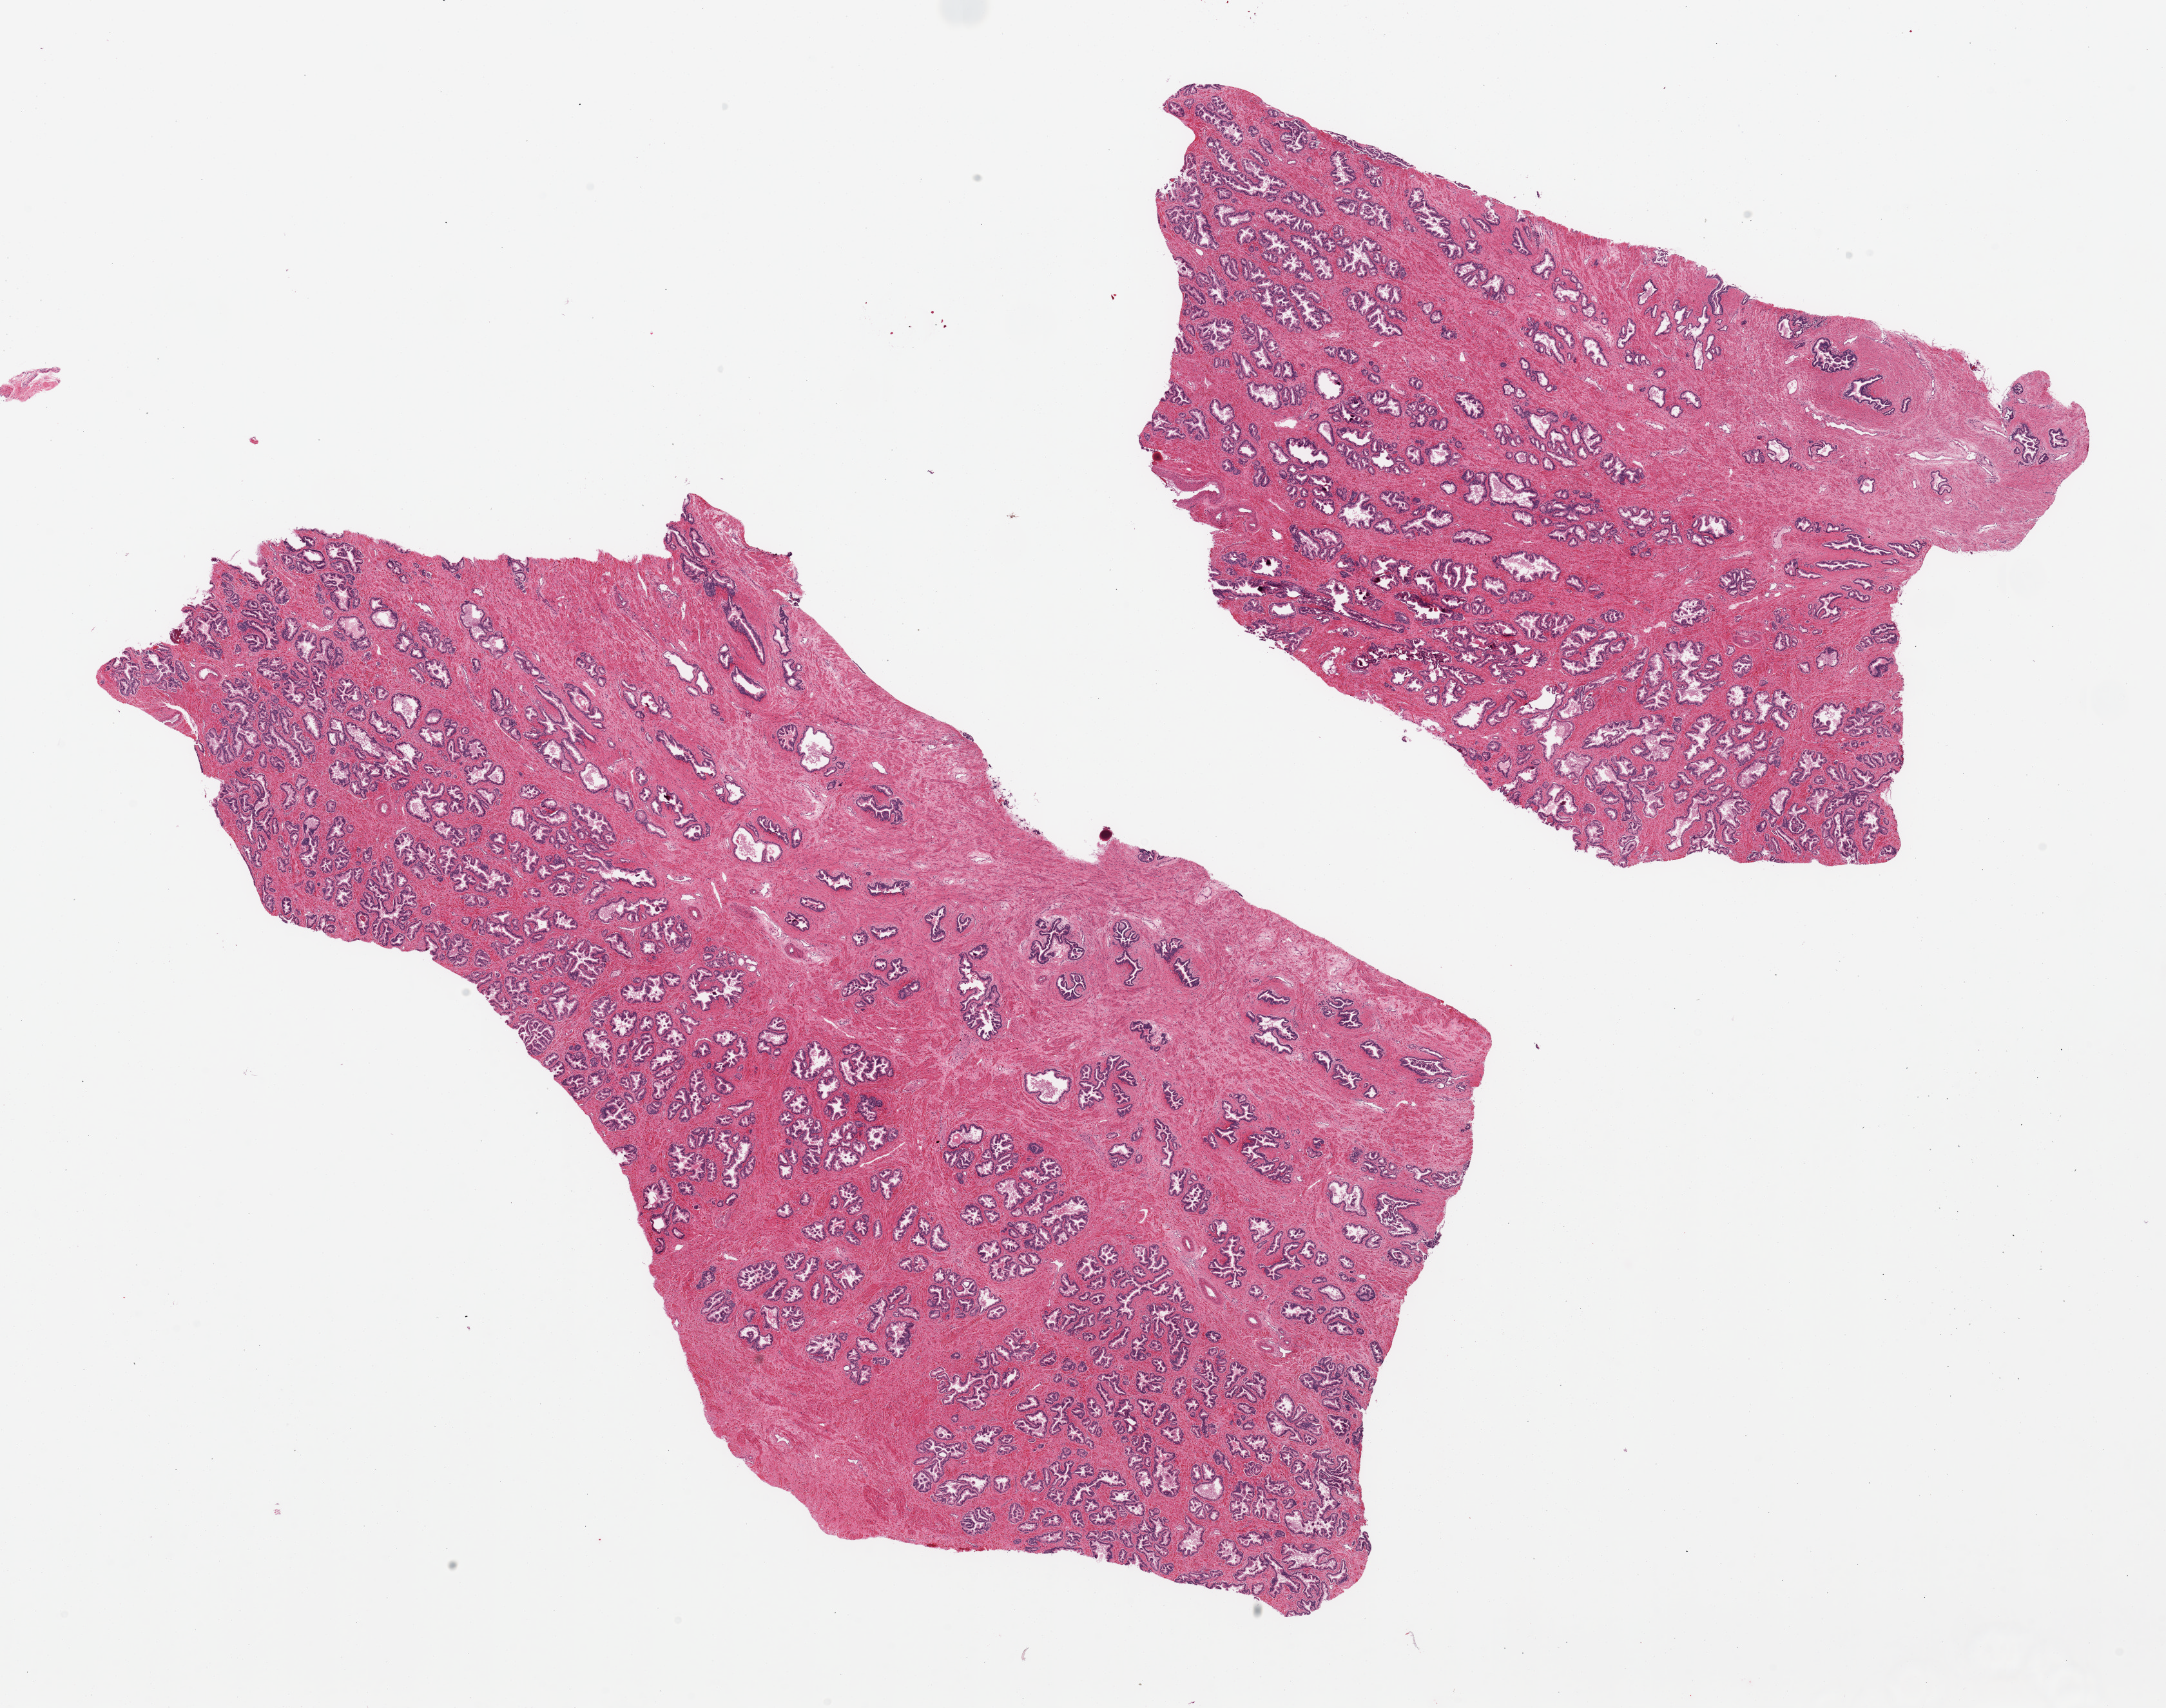
Digitized H&E-stained section, whole scanned area (about 26.6 x 21.0 mm) shown as a low-resolution overview, PAXgene-fixed, paraffin-embedded tissue, section of prostate (target tissue), donor tissue sample. Donor: male.
Reviewer comment on this tissue sample: 2 pieces; good admixture of glands/stroma.